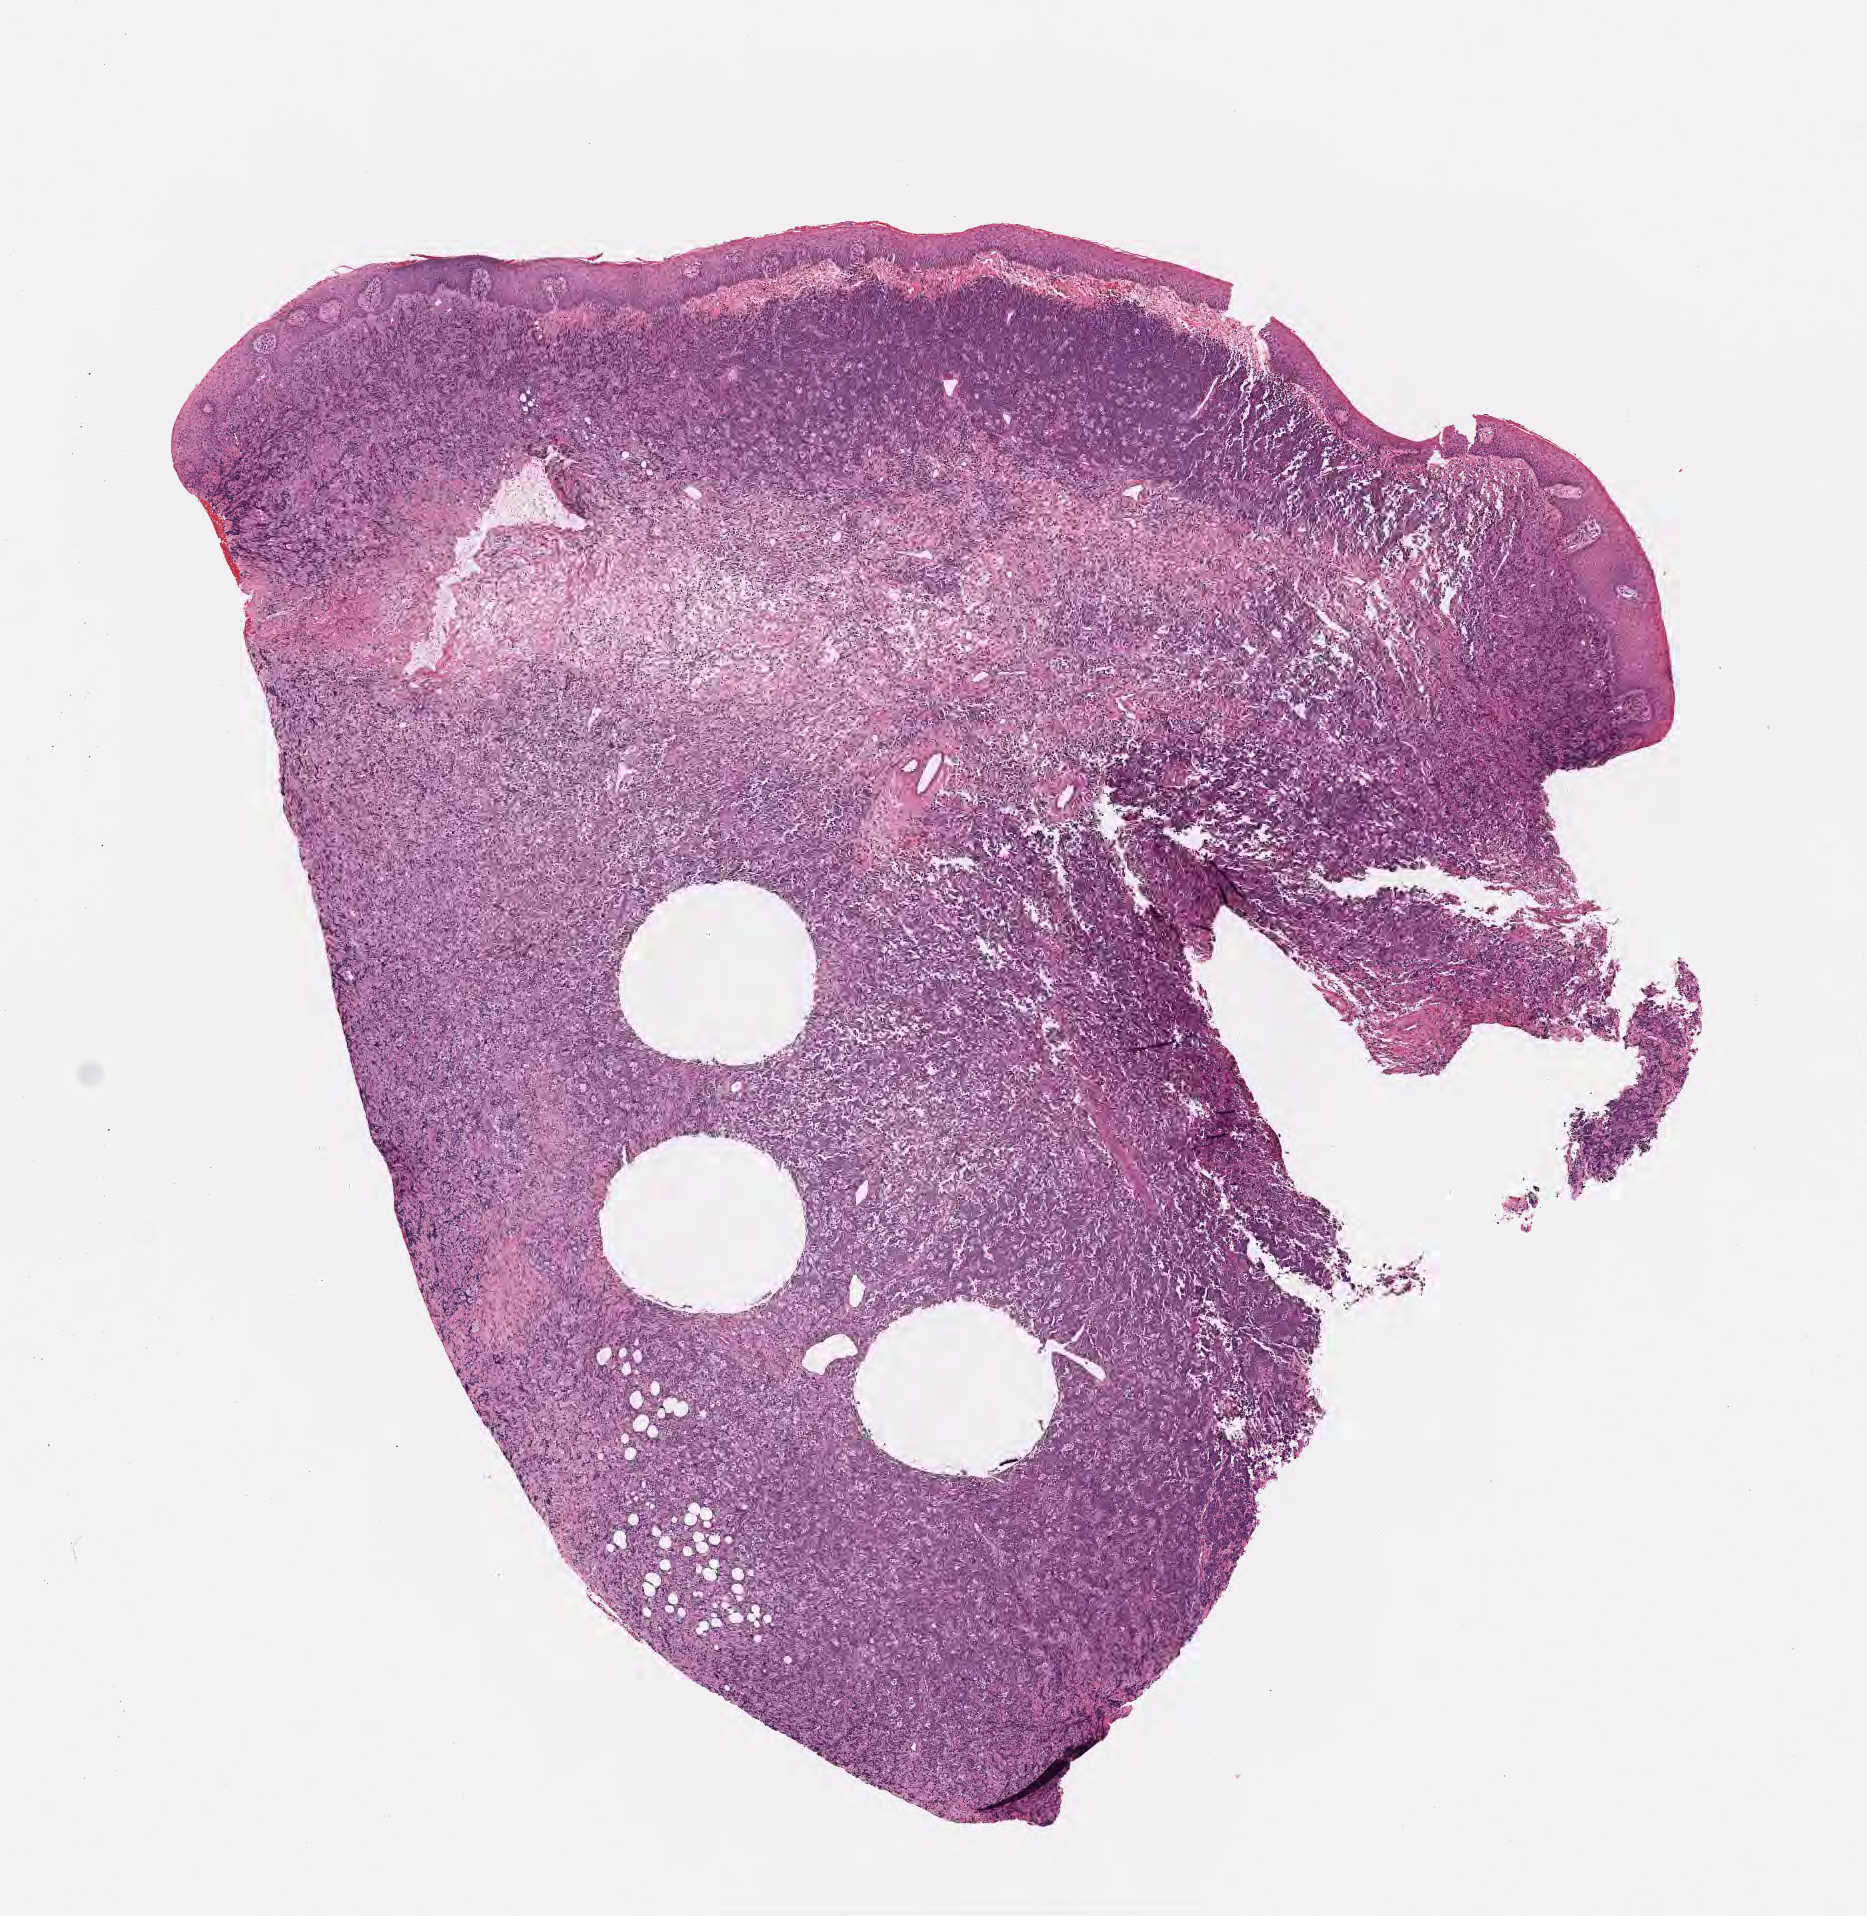
Digitized hematoxylin and eosin (H&E)-stained section, low-resolution overview of the scanned area, about 7.5 x 7.7 mm. Formalin-fixed paraffin-embedded section. Primary tumor. Anatomic site: cranium. Male patient; age at initial diagnosis 5 years. Slide review estimates, as recorded: tumor cells 70%, tumor nuclei 90%, stromal cells 10%, necrosis 10%, normal cells 10%. Inflammatory infiltration, as recorded: lymphocyte infiltration 40%, monocyte infiltration 30%, neutrophil infiltration 10%.
- Ann Arbor stage (patient): Stage IV
- diagnosis: Diffuse large B-cell lymphoma, NOS
- section: bottom of the tissue portion